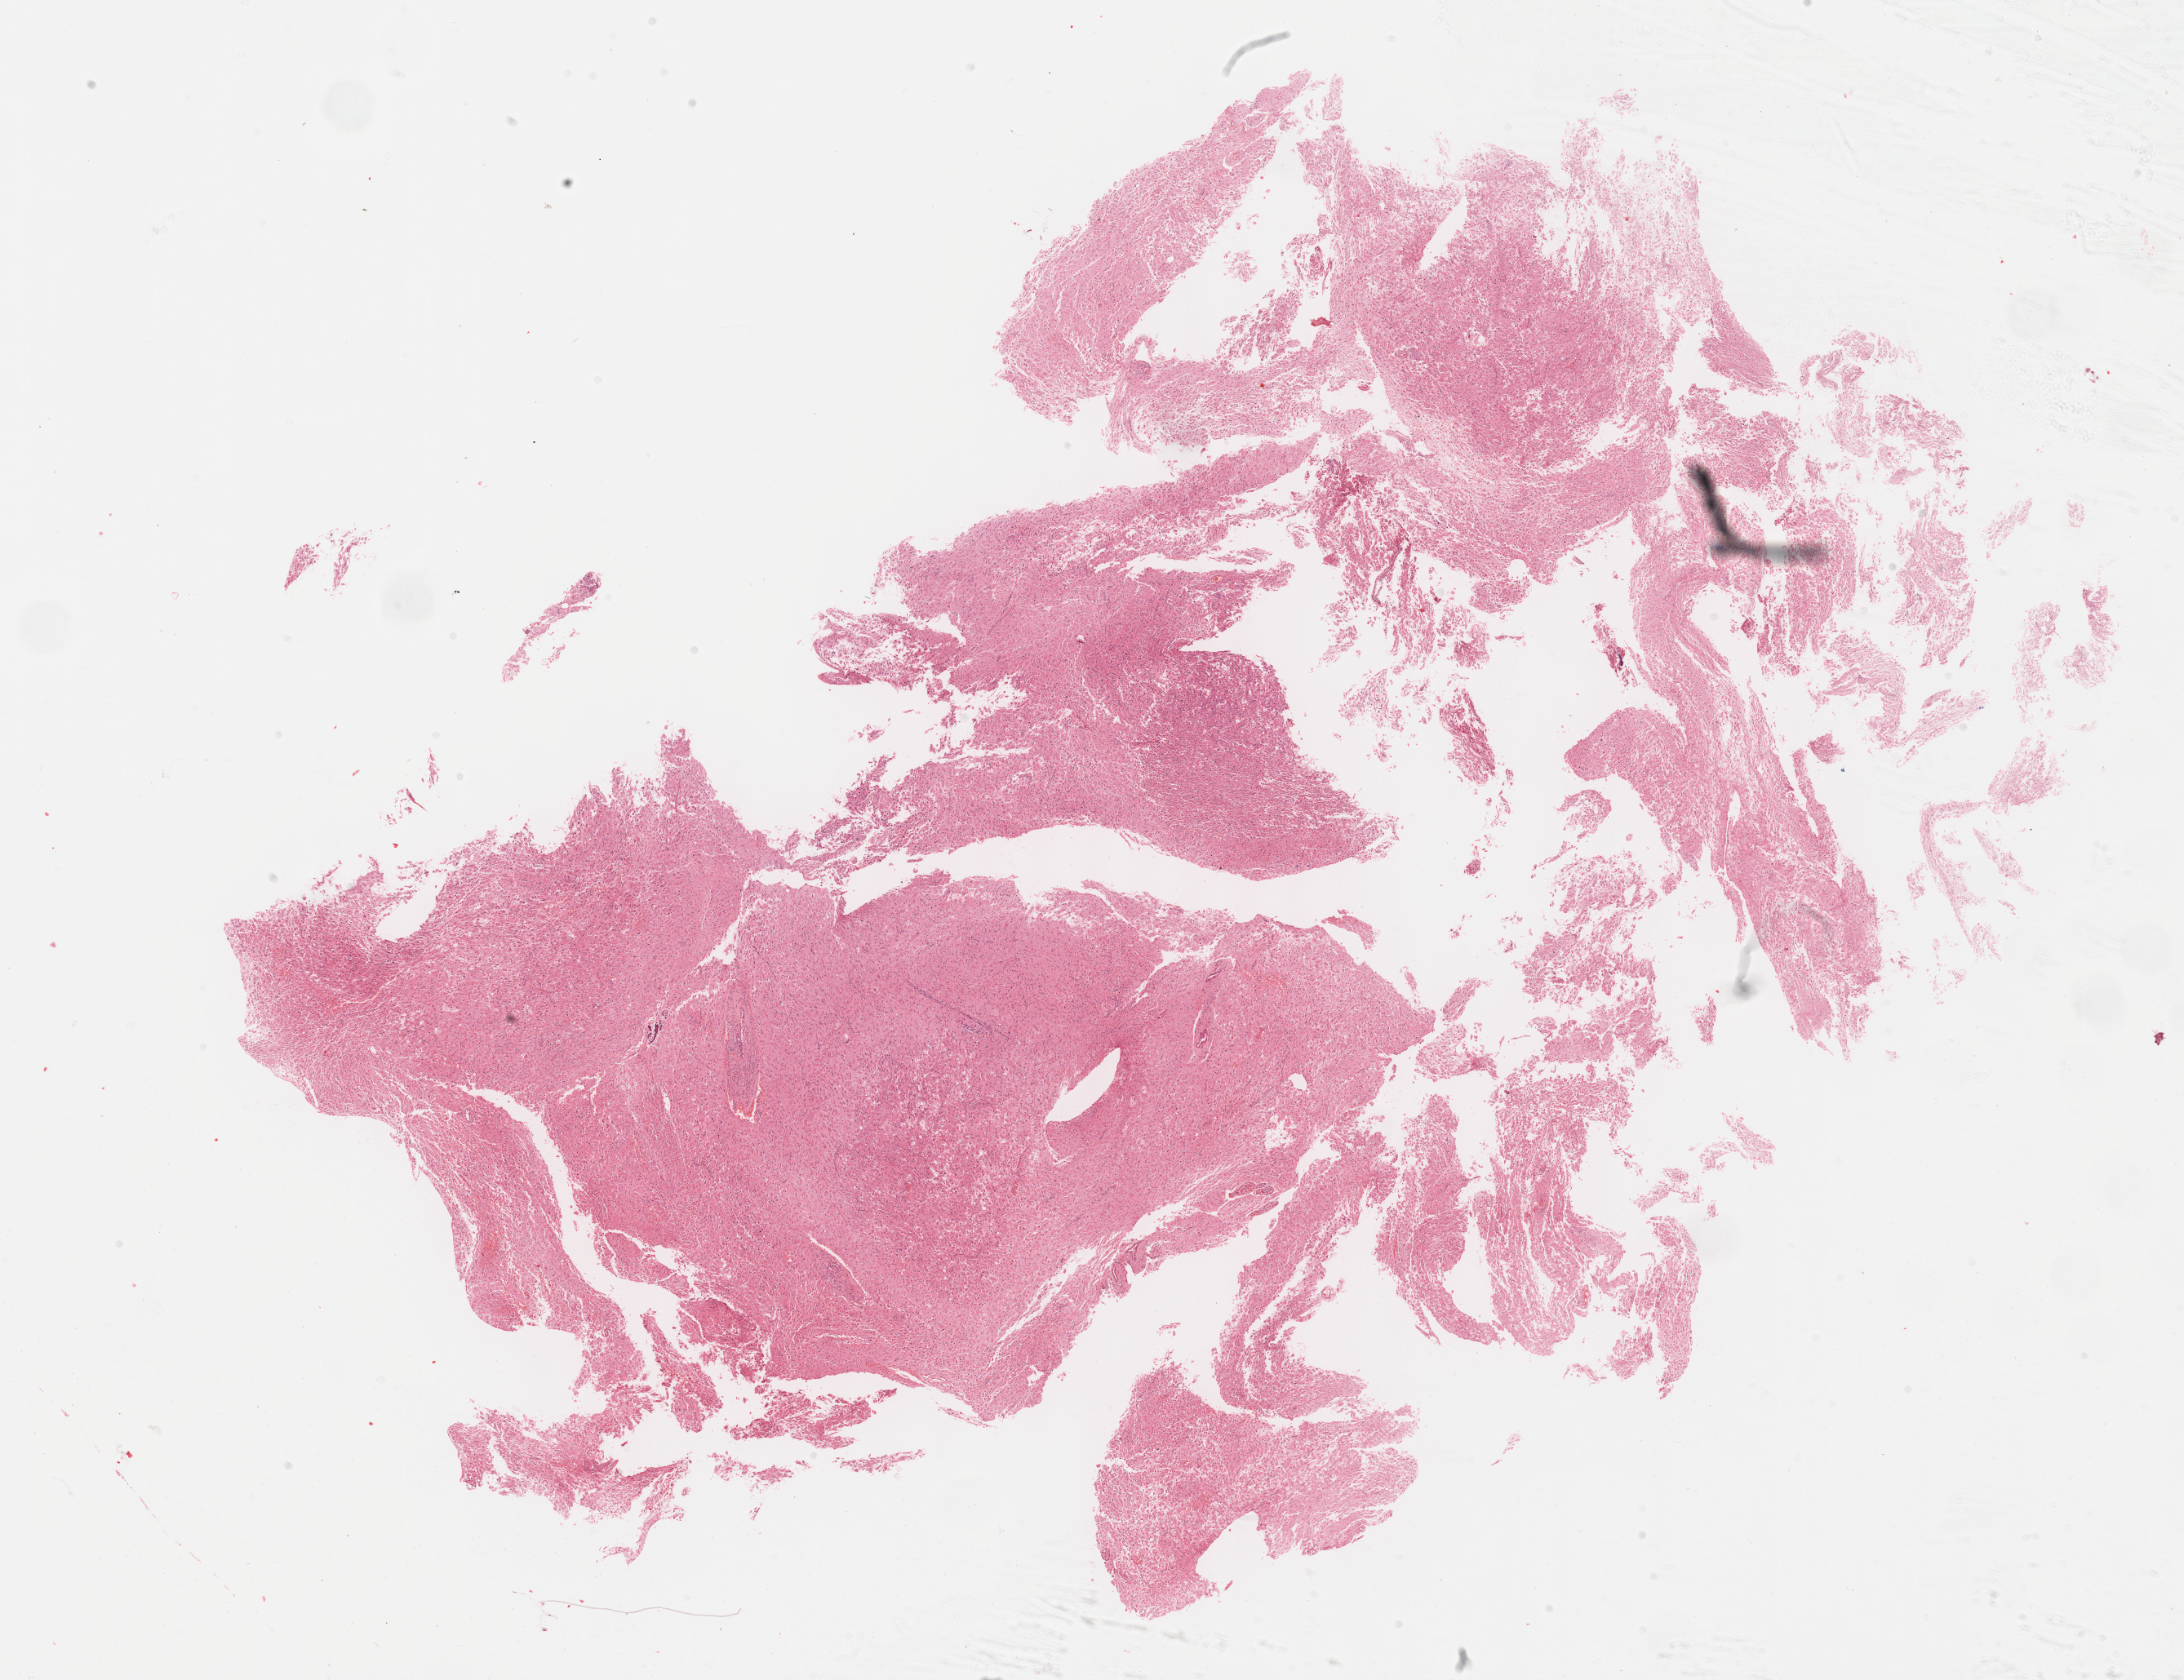
H&E-stained whole-slide image, whole scanned area (about 21.6 x 16.7 mm, from a 40x scan) shown as a low-resolution overview, FFPE section, sample: primary tumour, brain. Patient: male, age at initial diagnosis 27 years. Histologic grade: G2 (moderately differentiated).
Diagnosis: Astrocytoma, NOS (cerebrum). Laterality: left.